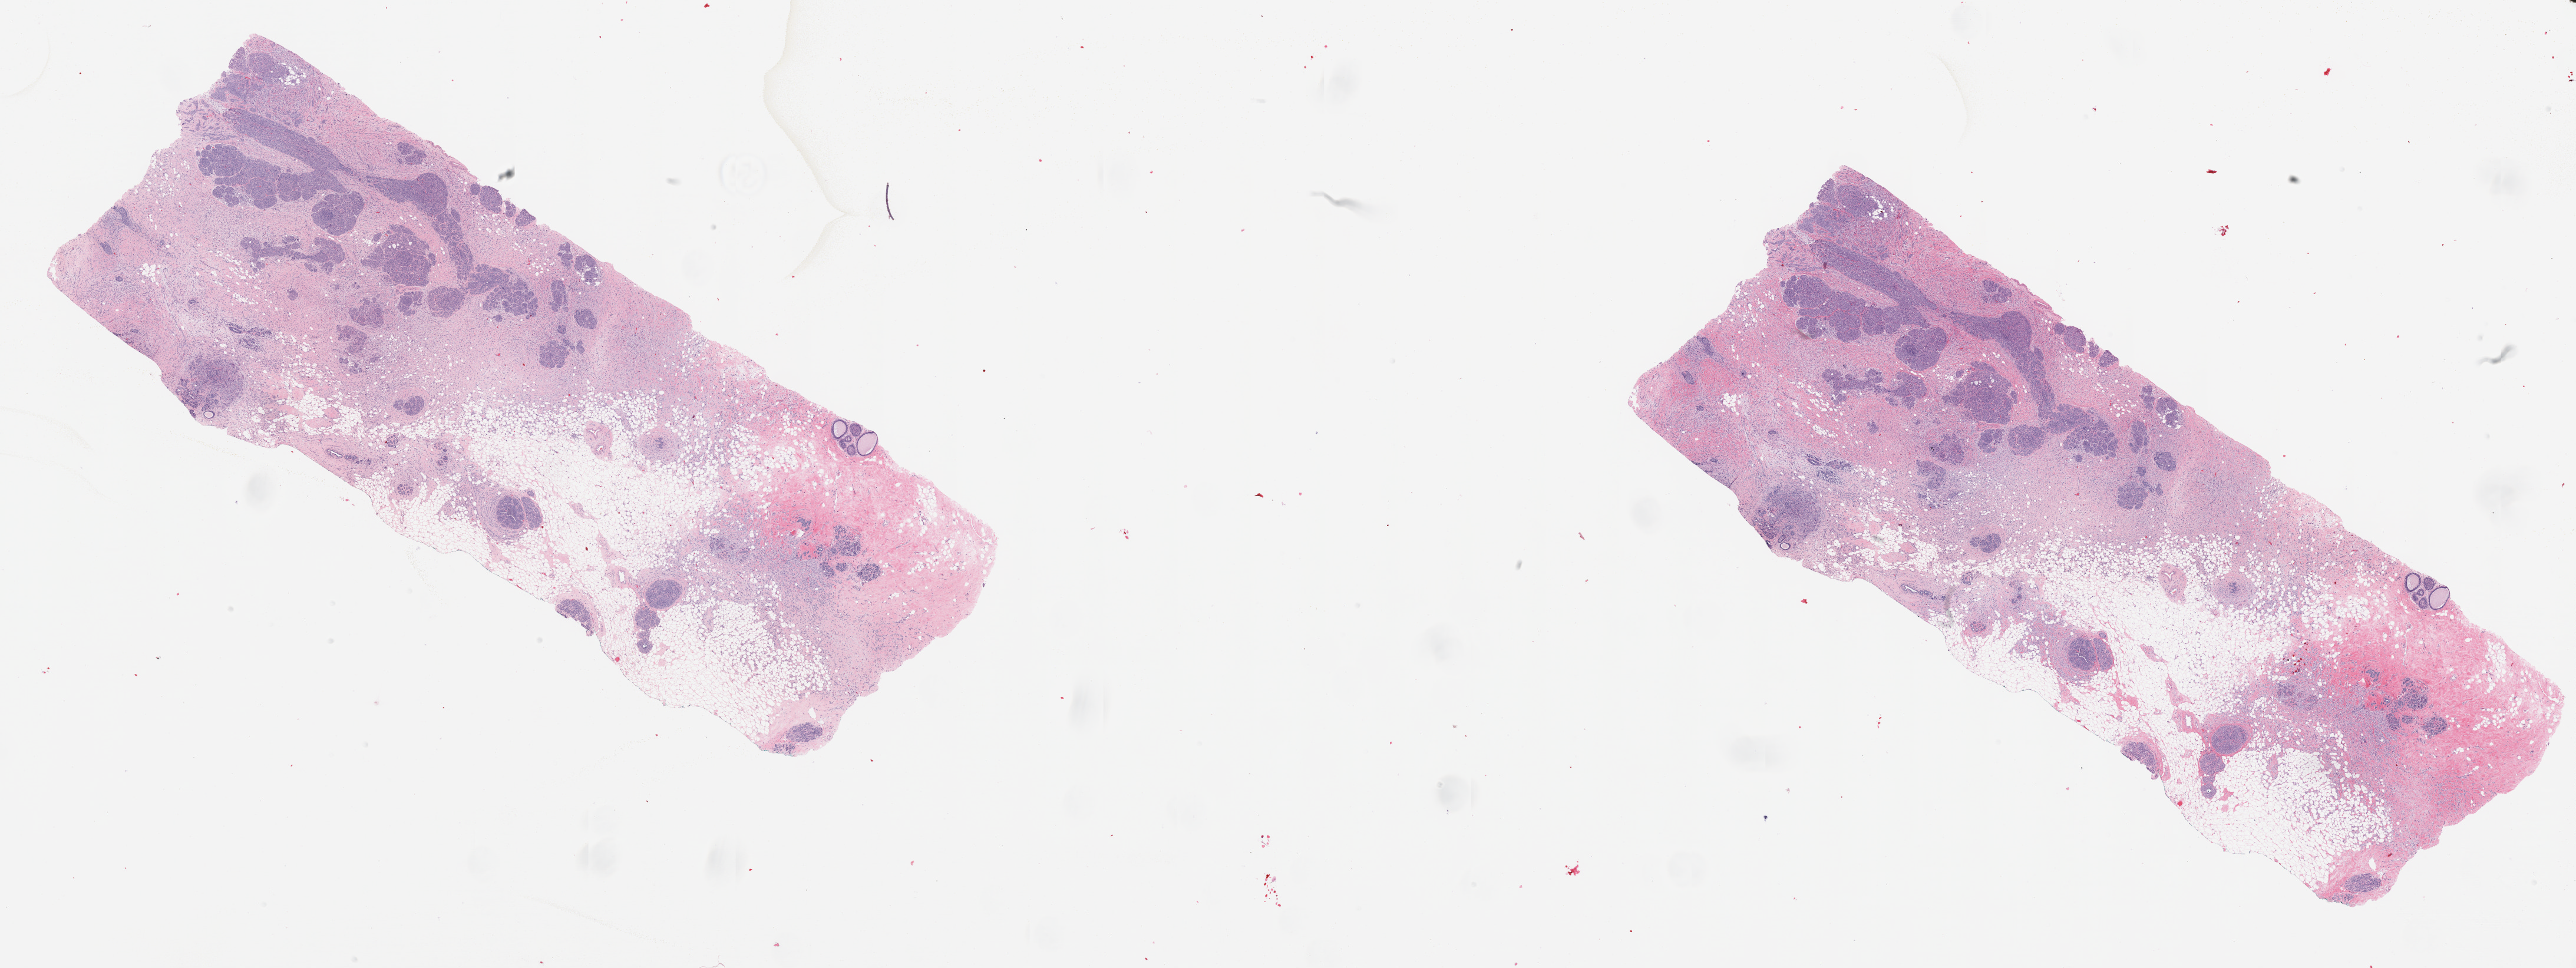
Whole-slide histology image, H&E — whole scanned area (about 35.0 x 13.2 mm, slide scanned at 20x) shown as a low-resolution overview. Formalin-fixed paraffin-embedded (FFPE) diagnostic section. Sample: primary tumour, breast. Female, age 45 years at initial diagnosis.
- lymph nodes positive (case pathology): 2 of 10 examined
- AJCC pathologic stage: IIB
- pathologic diagnosis: Lobular carcinoma, NOS